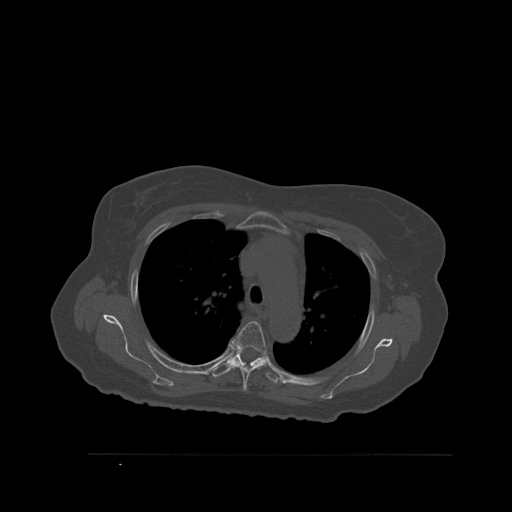
CT including the spine, one axial slice; position 403 of 527 along the scan axis; bone window (W 1800 / L 400 HU); 512 × 512 image matrix, field of view 470 × 470 mm. Patient: female, 73 years. From the clinical record (not read from this slice): primary cancer: breast; vertebrae with lytic lesions (as recorded): L2.
Annotated regions visible in this slice (semi-automatic segmentation, software-assisted and operator-edited):
- T4 vertebra: bounding box <230,321,268,391> (left, top, right, bottom; pixels)
- T5 vertebra: <211,346,279,385>